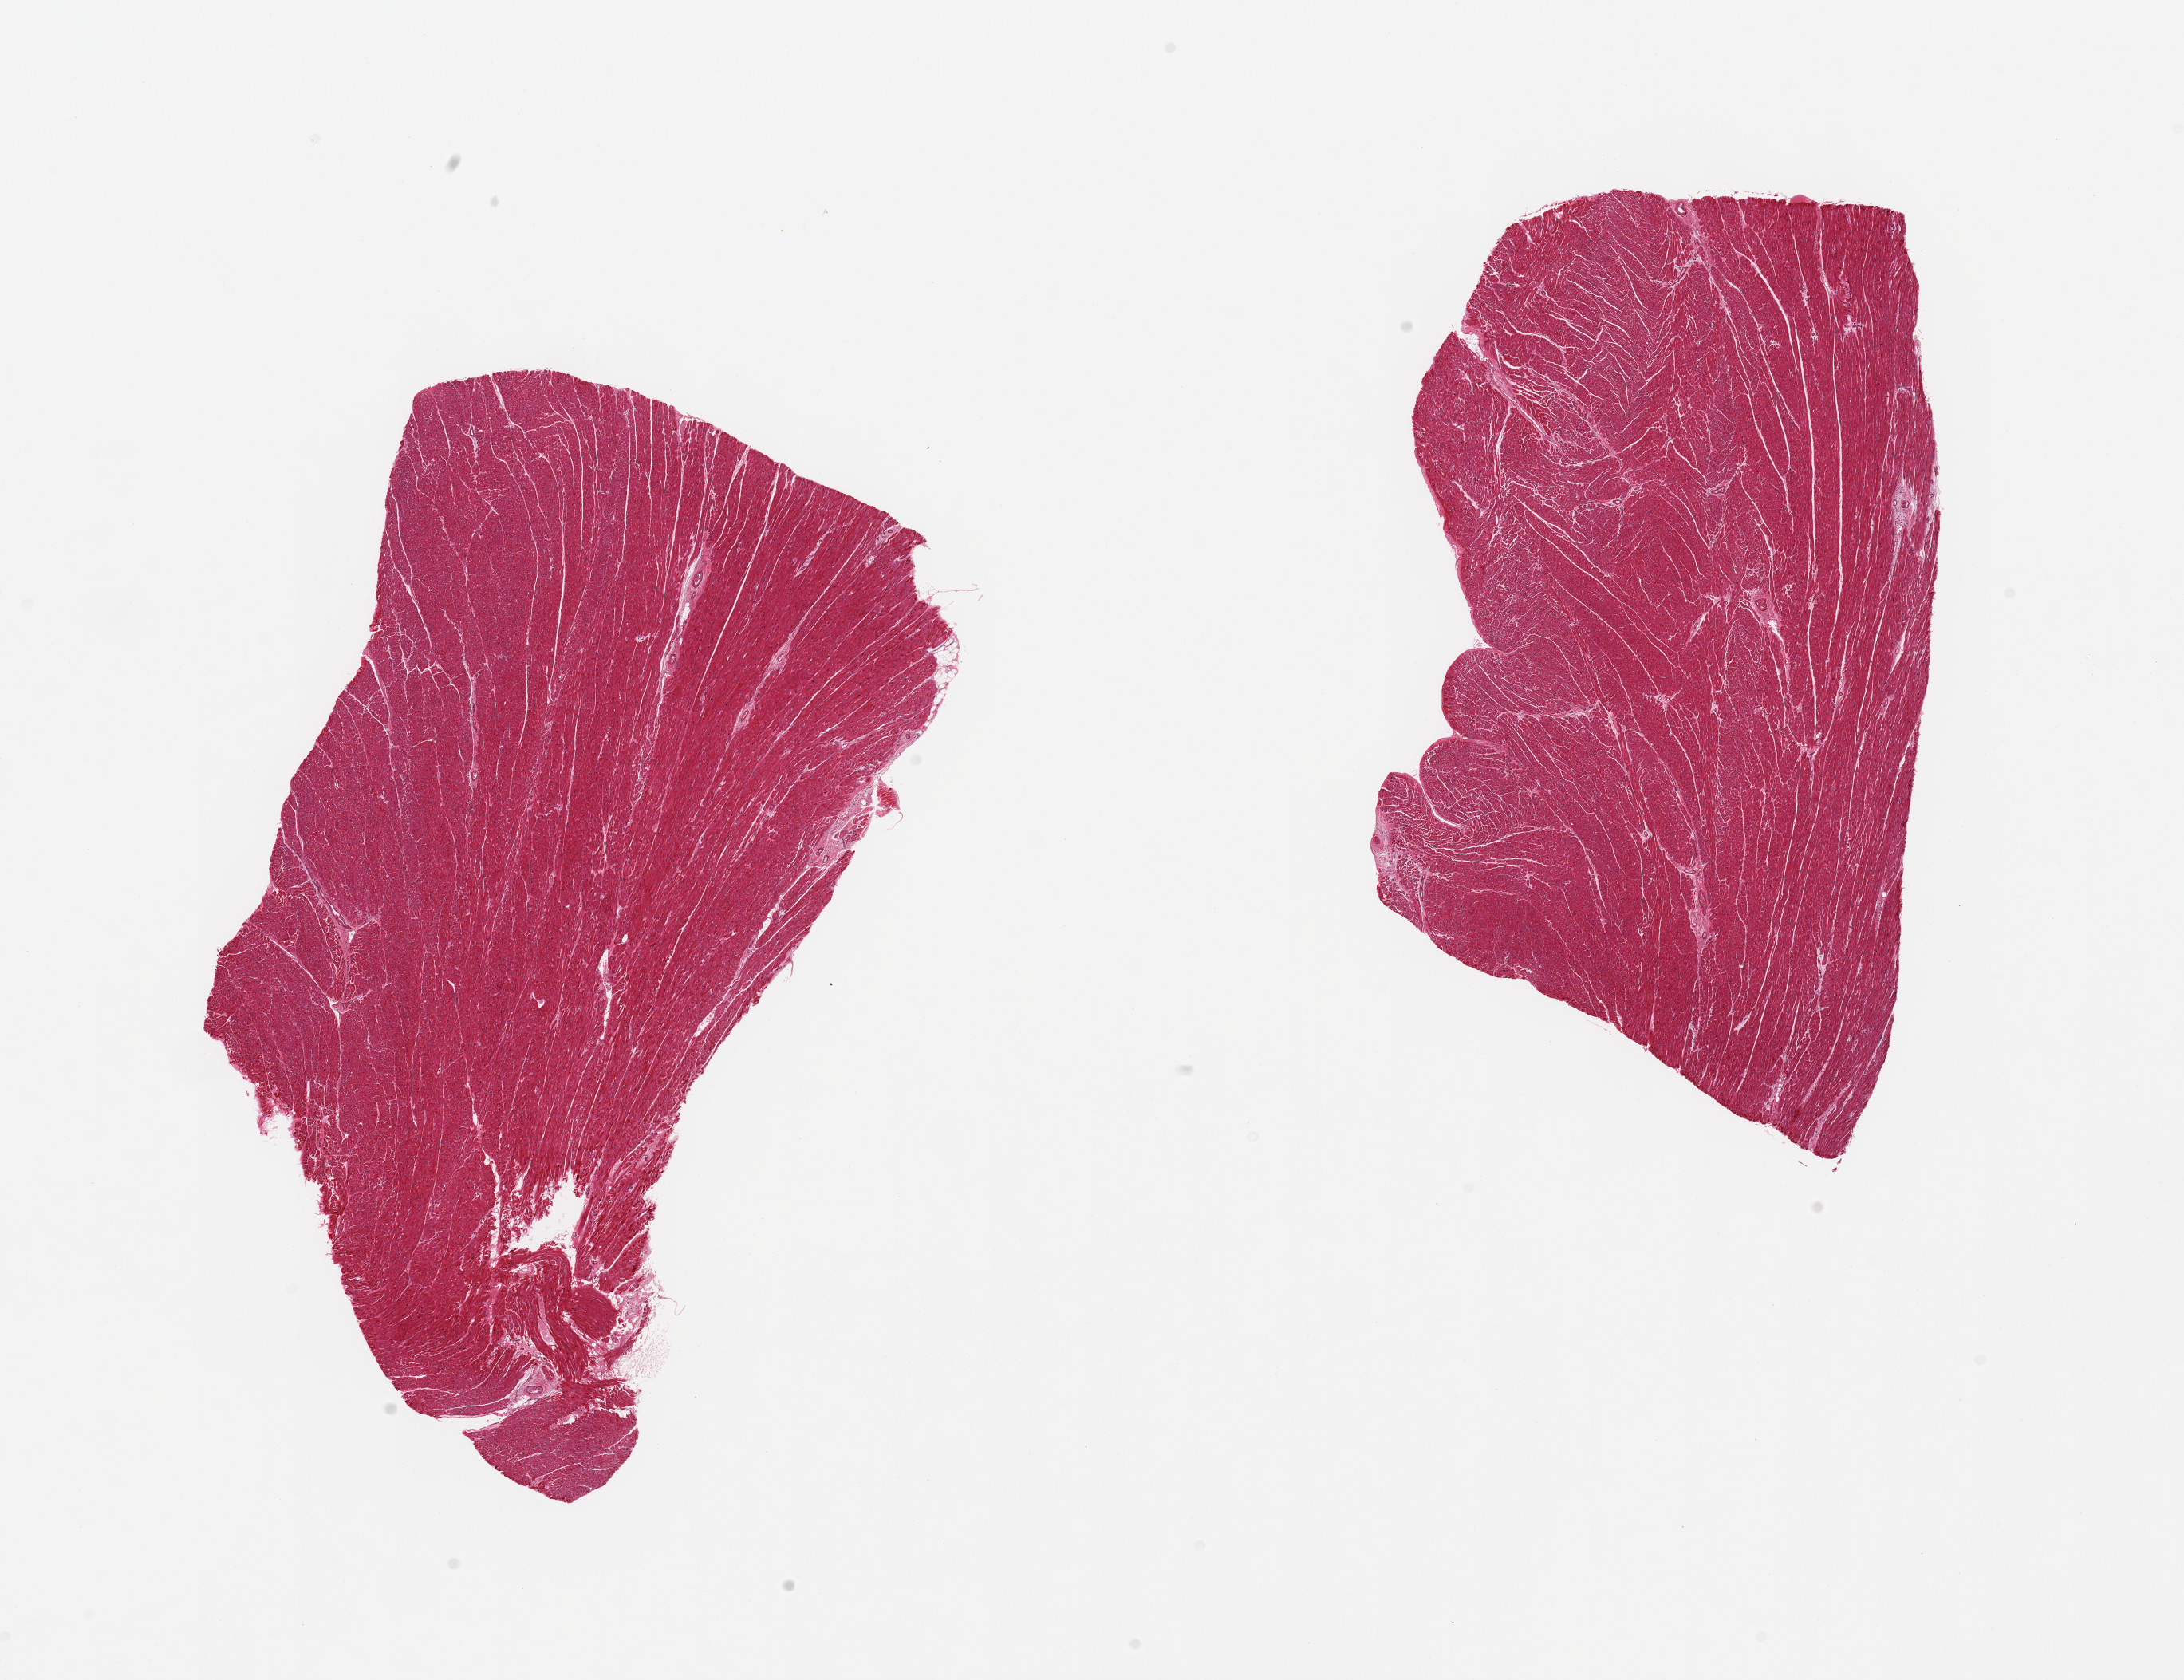
Whole-slide image, haematoxylin and eosin stain, a low-resolution overview of the entire scanned area, about 21.7 x 16.7 mm, PAXgene-fixed paraffin-embedded (PFPE) section, section of heart (target tissue), tissue donor sample. Donor sex: male.
Pathologist's review note for this sample: 2 pieces, minimal fibrosis.